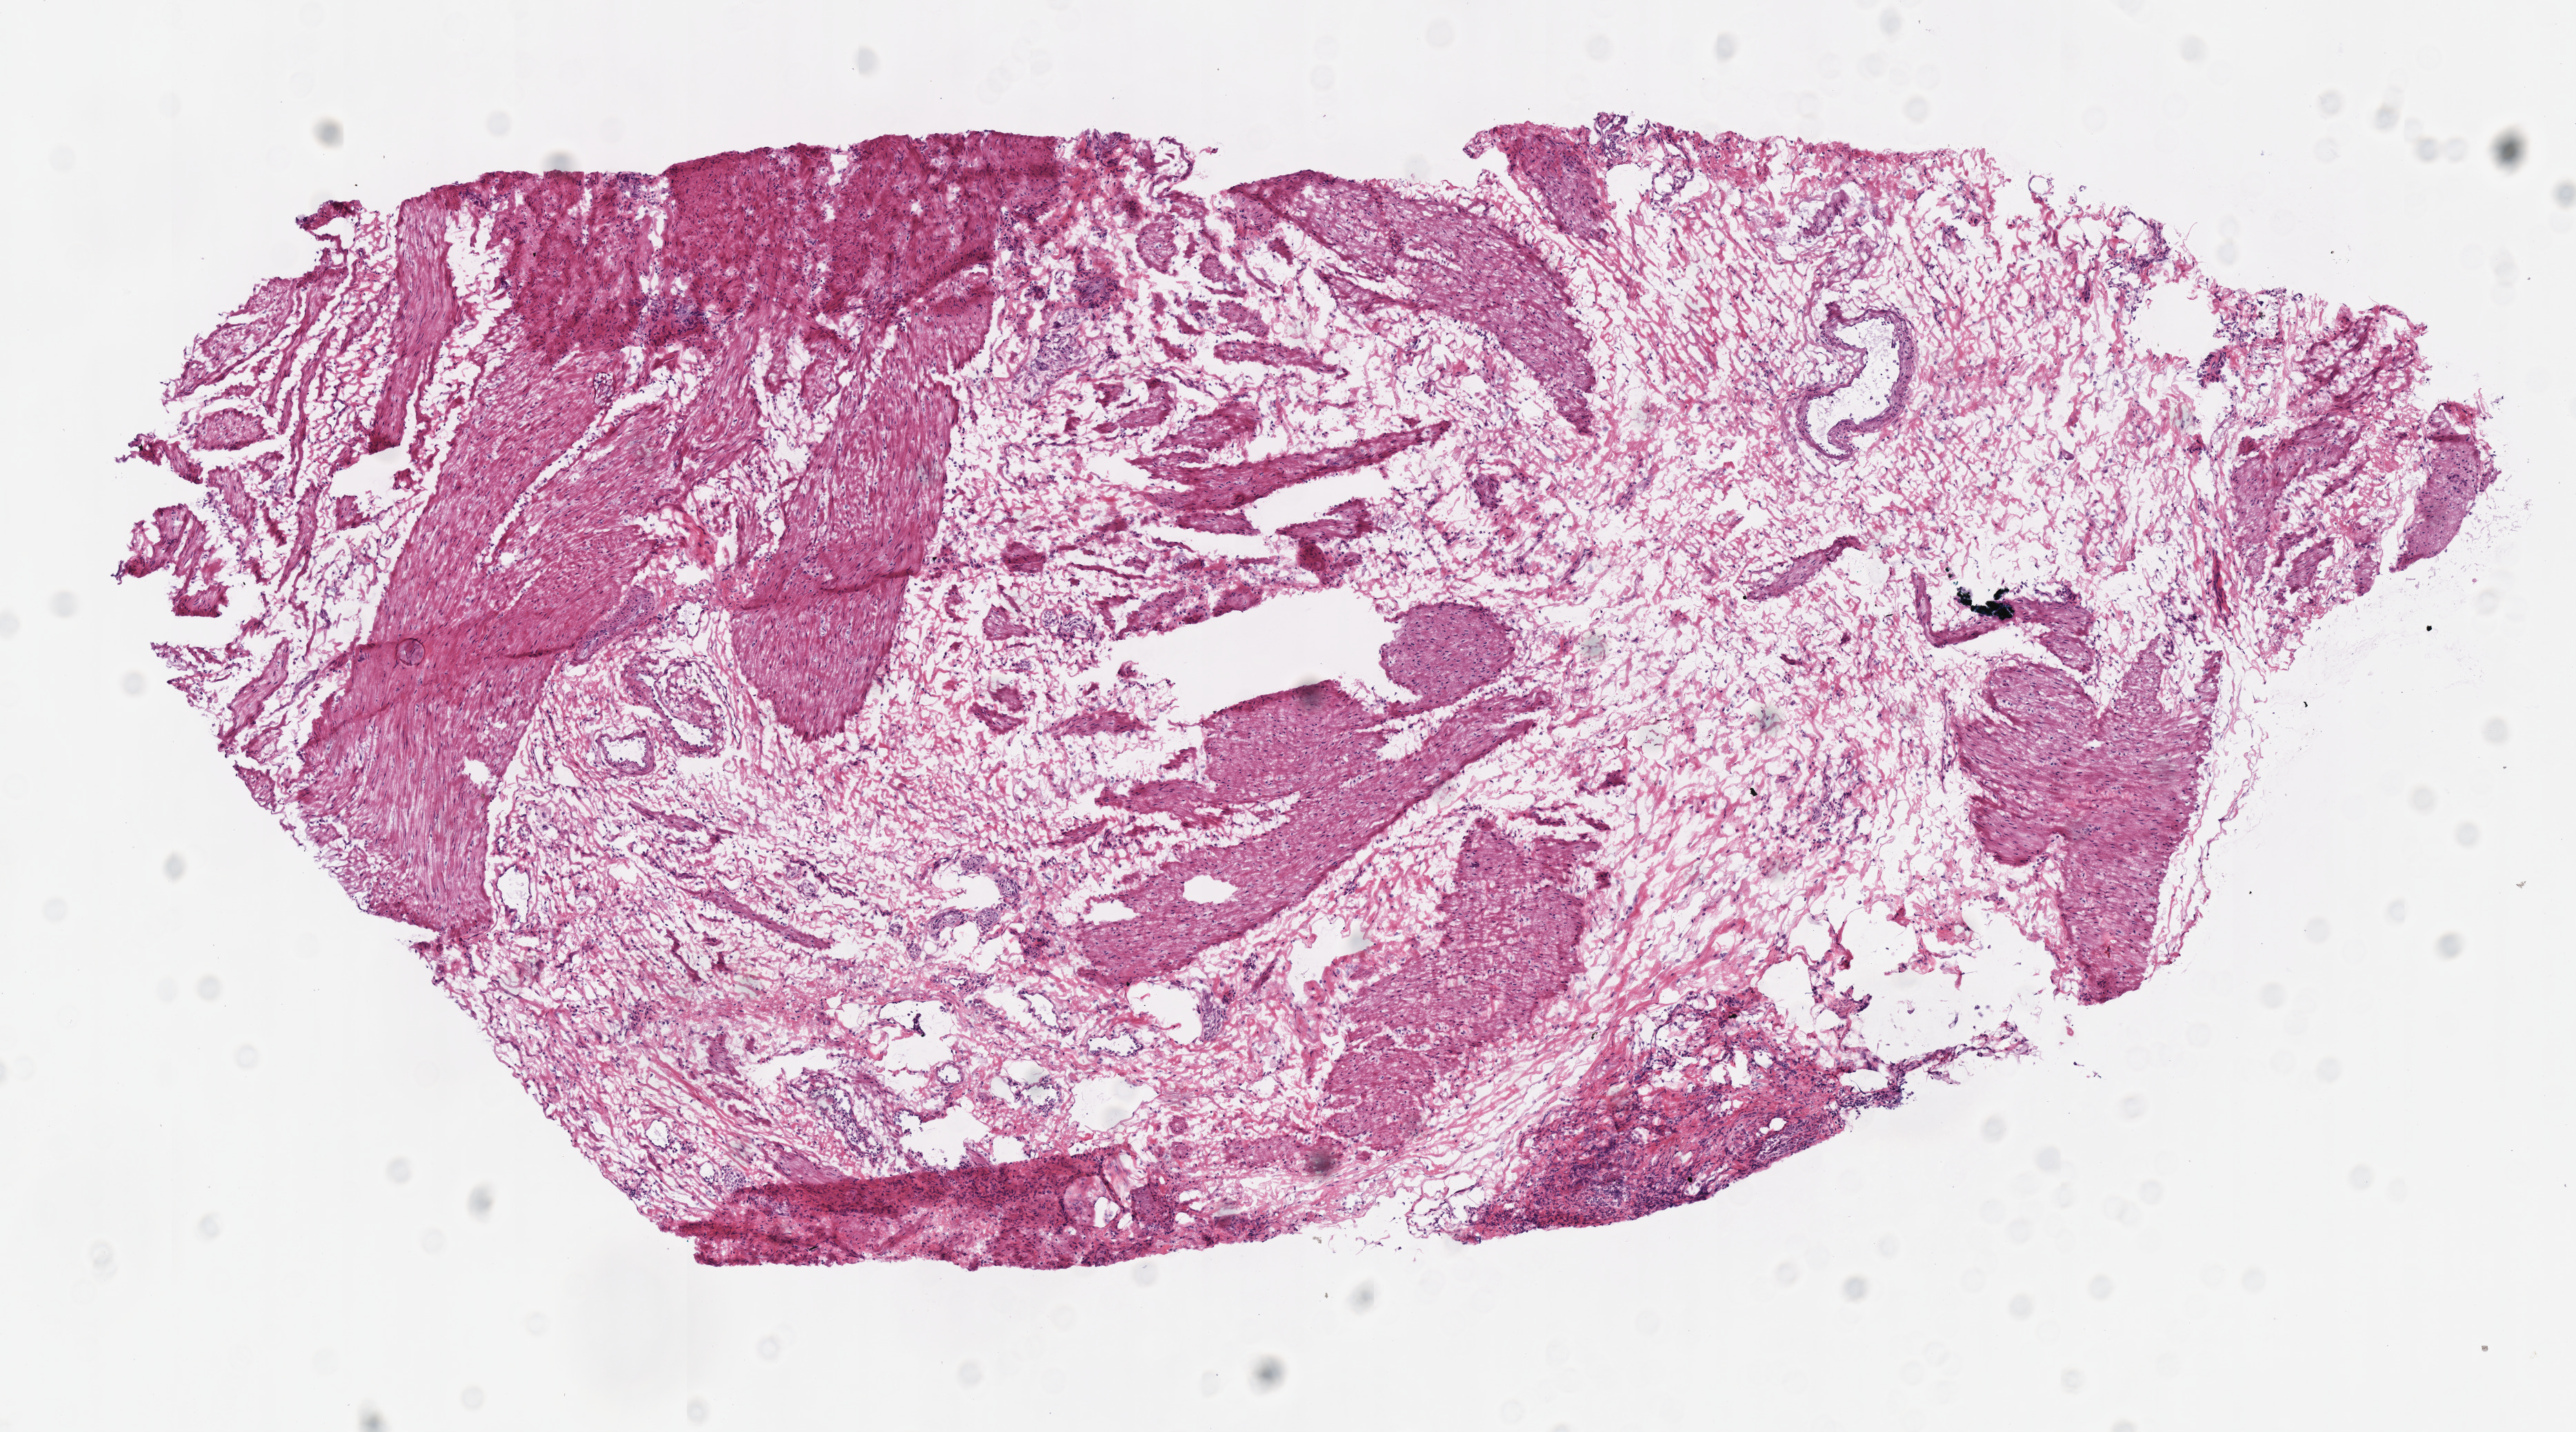
Digitized Hematoxylin and eosin (H&E) stained tissue section (whole slide) — low-resolution overview of the scanned area, about 7.3 x 4.1 mm. Frozen section from the top of the tissue portion. Solid tissue normal (non-tumour tissue) sample from the stomach. Male, age 77 years at initial diagnosis.
* this section: solid tissue normal (non-tumour) sample from the same patient
* patient diagnosis: Adenocarcinoma, NOS (cardia, NOS)